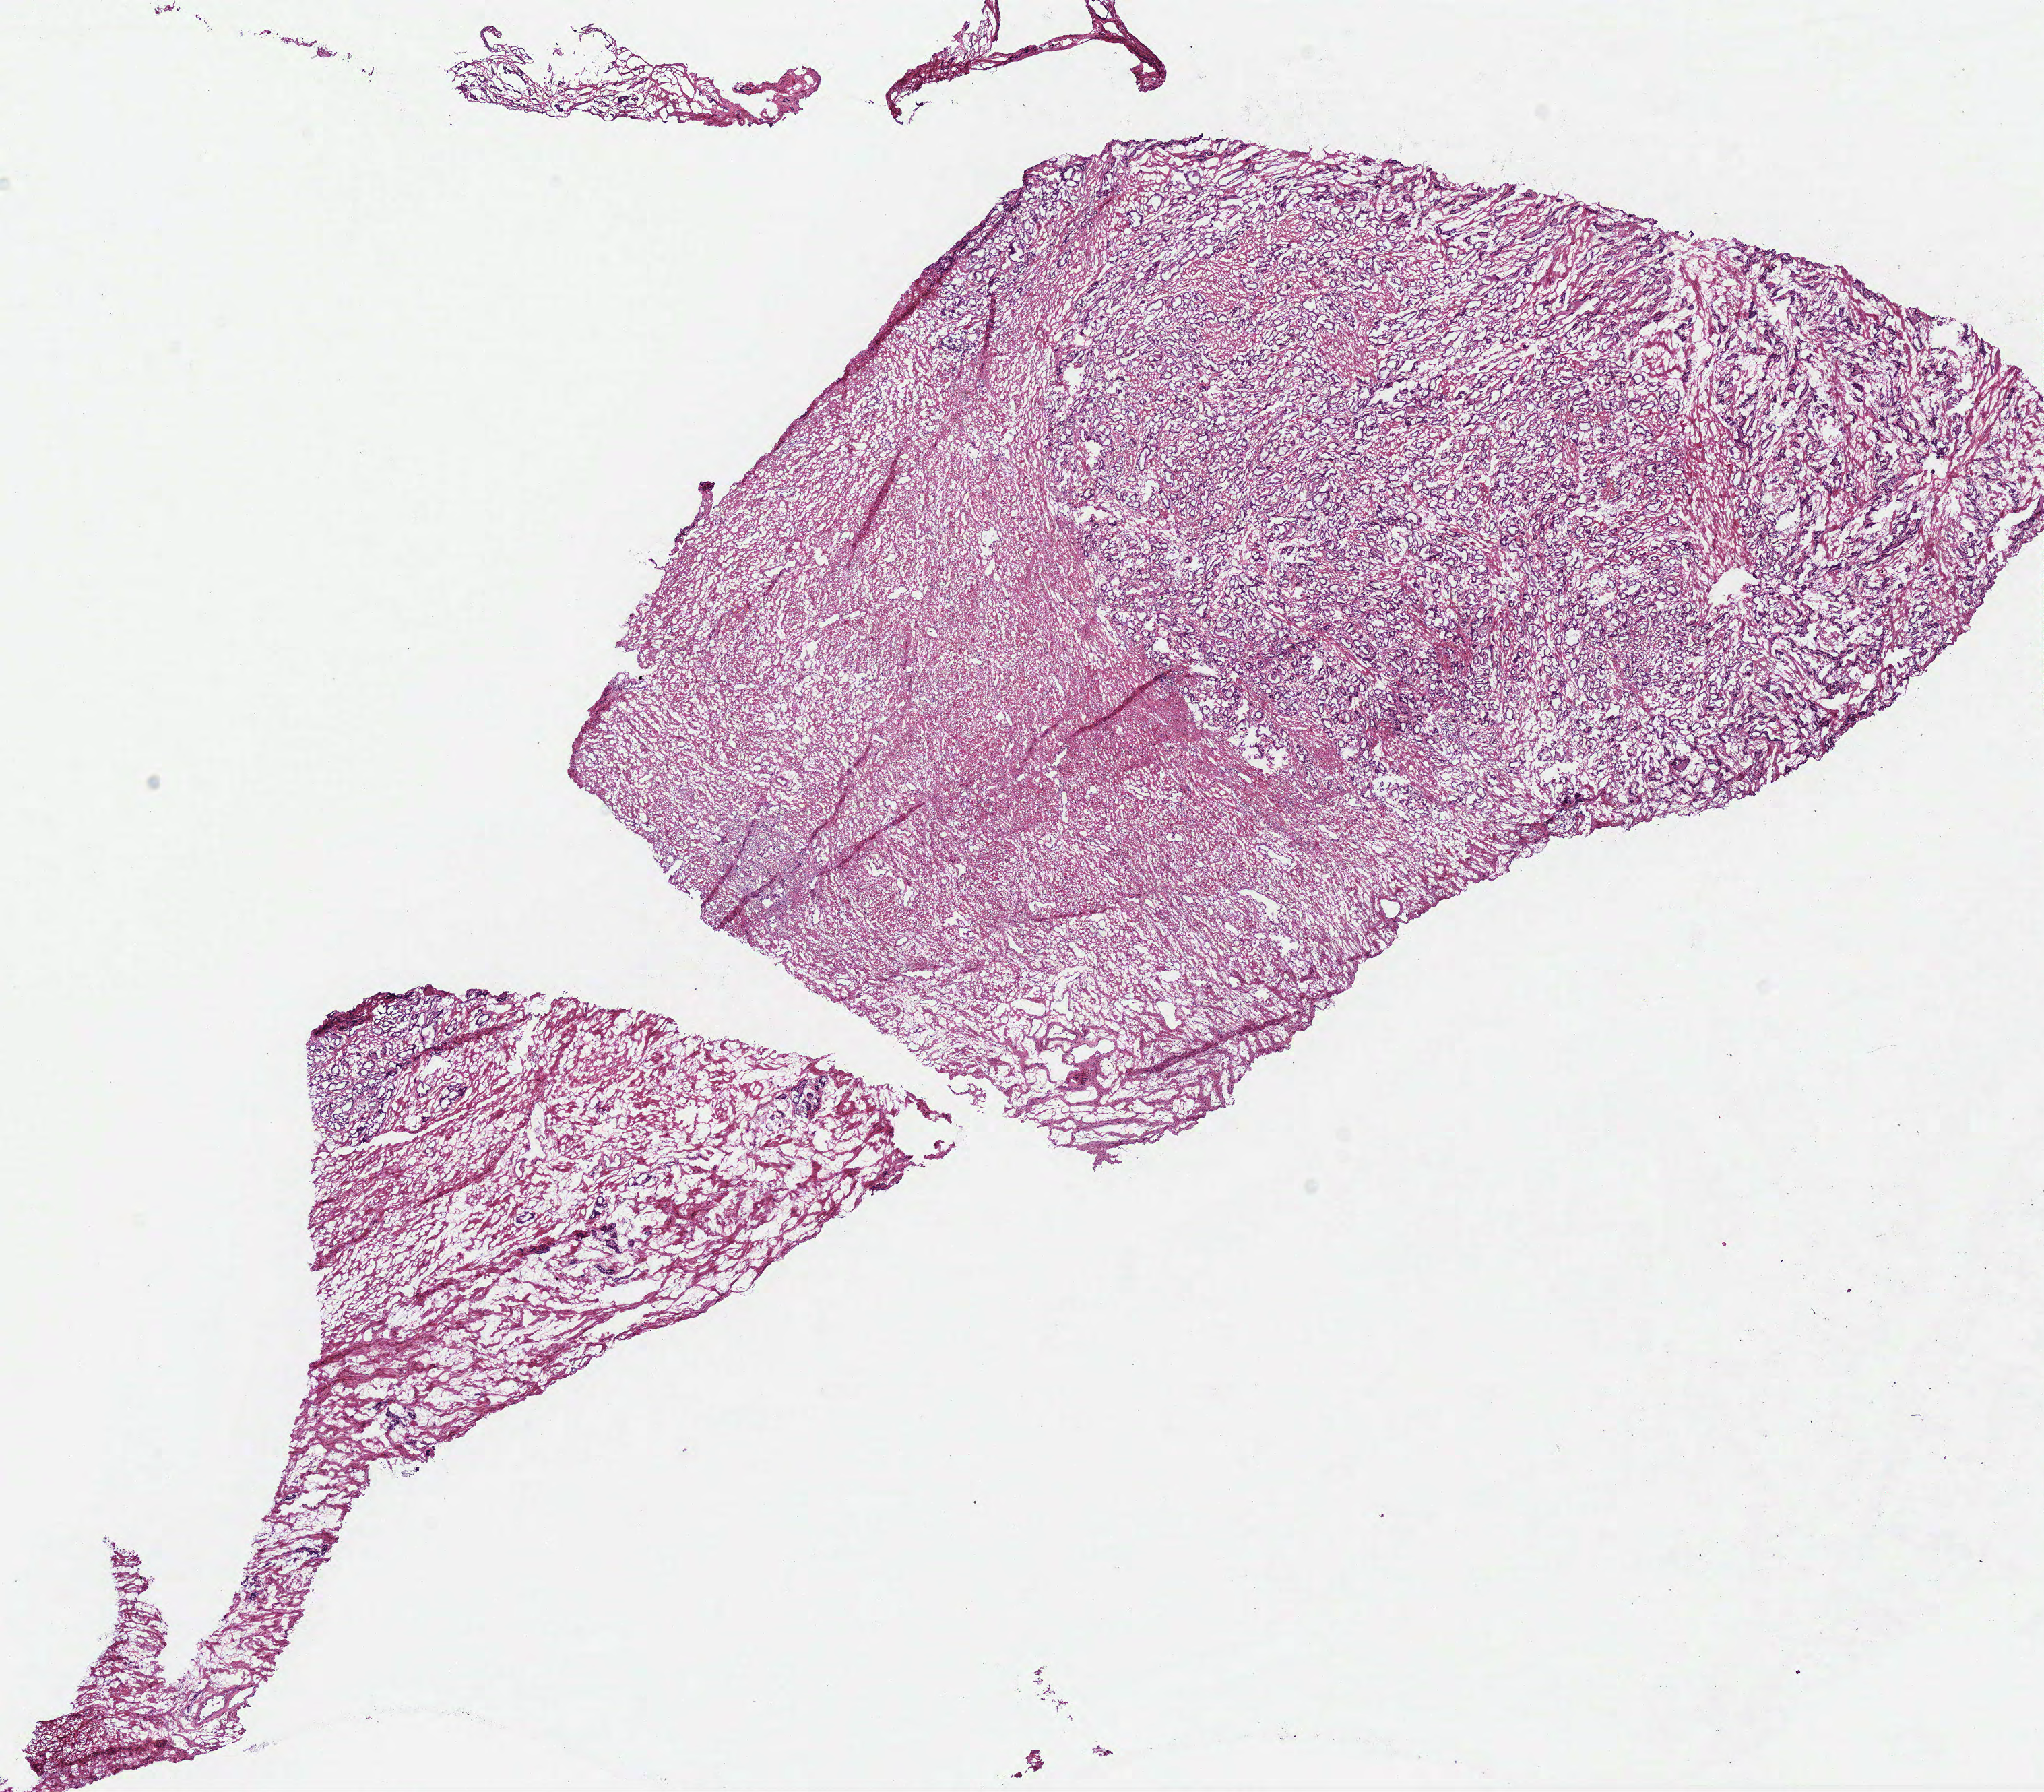
Whole-slide histology image, Hematoxylin and eosin (H&E) stained — low-resolution overview of the scanned area, about 12.0 x 10.5 mm, frozen section from the bottom of the tissue portion, primary tumour sample from the prostate. Male, age 55 years at initial diagnosis. Gleason score: 7 (3+4). Pathologist review of this section (percent, as recorded): tumour cells 60%, tumour nuclei 70%, normal cells 0%, stromal cells 40%, necrosis 0%.
Pathologic diagnosis: Acinar cell carcinoma (prostate gland). Lymph nodes positive (case pathology): 0 of 4 examined. Laterality: bilateral.